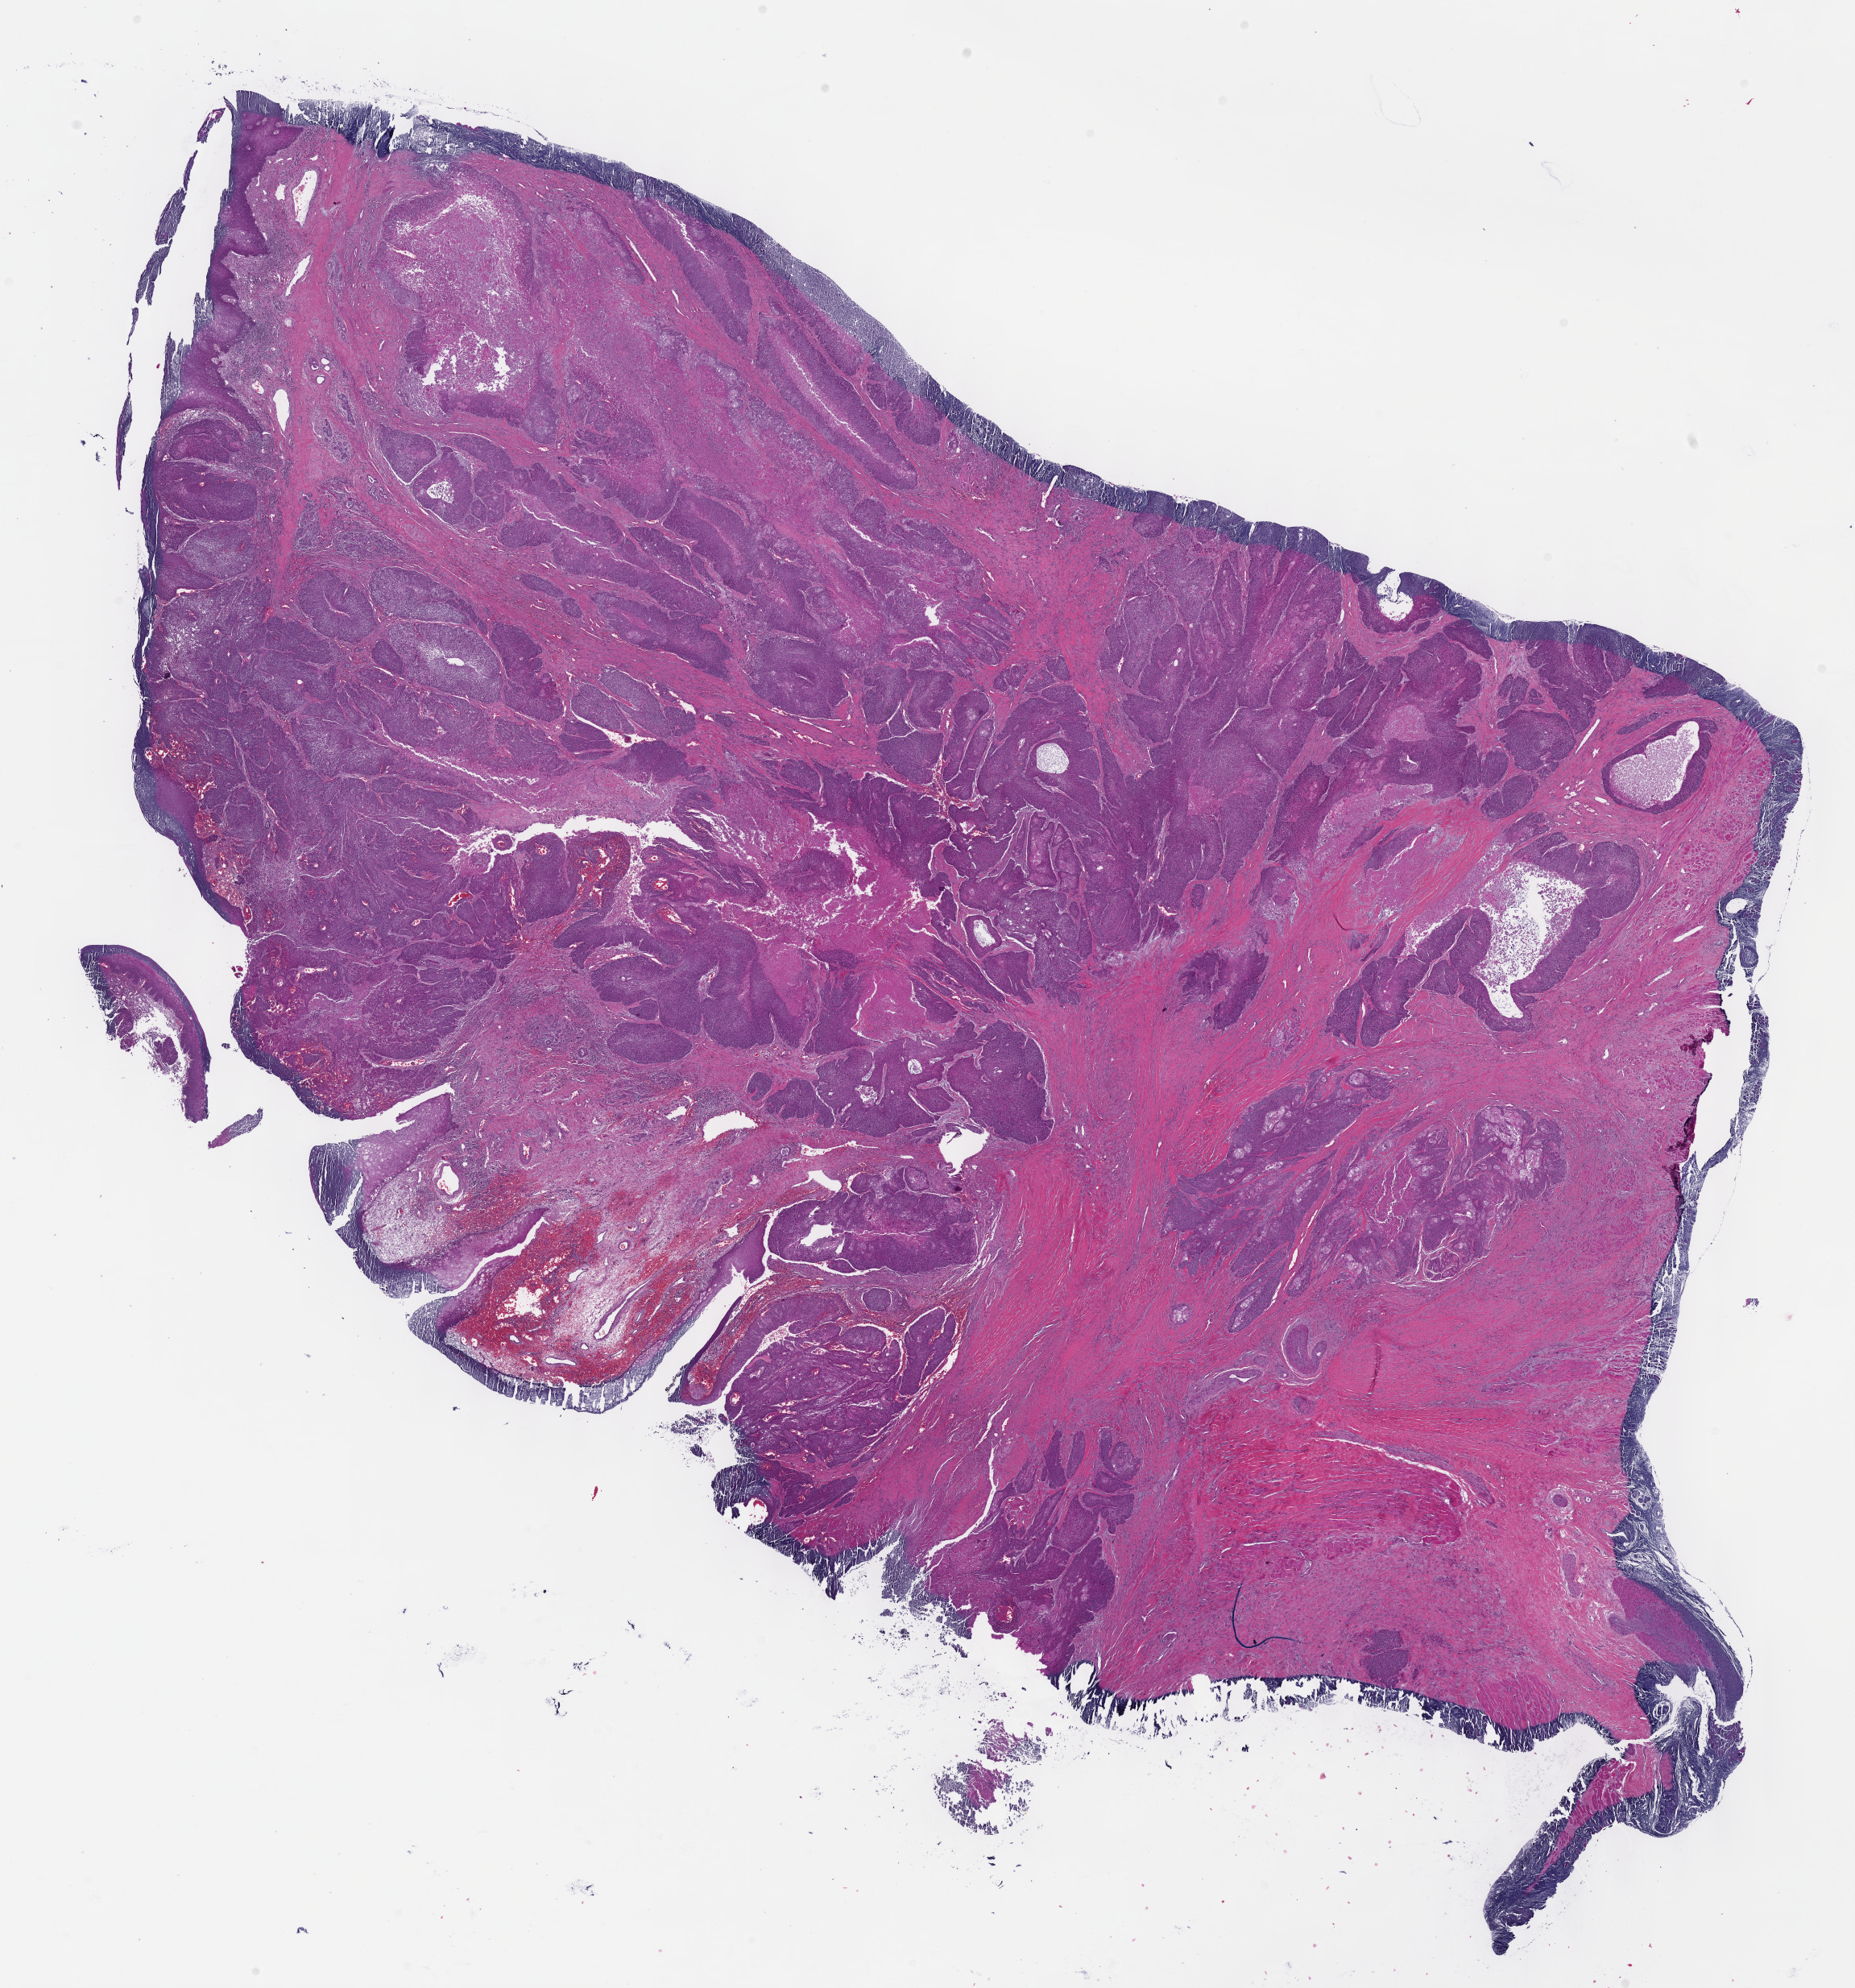
Whole-slide histology image, Hematoxylin and eosin (H&E) stained, a low-resolution overview of the entire scanned area, about 18.6 x 19.9 mm (from a 40x scan); formalin-fixed paraffin-embedded (FFPE) diagnostic section; sample: primary tumour, head and neck. Patient: male, age at initial diagnosis 58 years. Histologic grade: G2 (moderately differentiated).
• histologic diagnosis: Squamous cell carcinoma, NOS
• AJCC pathologic stage: IVA (7th edition)